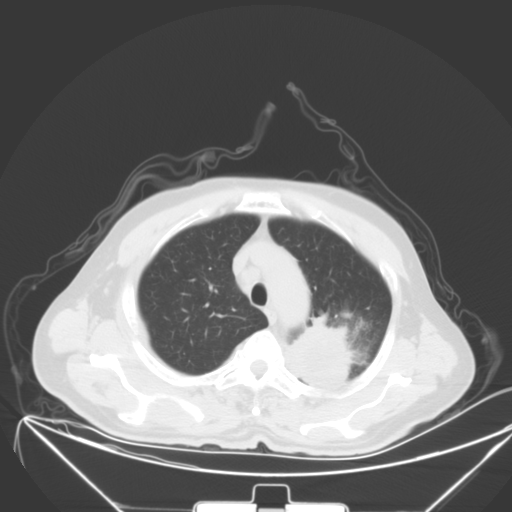
Chest CT, one axial slice; position 47 of 64 along the scan axis; 120 kVp; lung window (W 1500 / L -600 HU); 5 mm slice thickness; 512 × 512 image matrix, field of view 431 × 431 mm. Patient: male, 58 years. From the clinical record (not read from this slice): clinical TNM (as recorded): T2b N3 M1b.
Annotated regions visible in this slice (rectangle marked by the reading radiologist):
- lung tumour (recorded histology: adenocarcinoma): bounding box (x1, y1, x2, y2) in pixels: (286, 310, 355, 402)